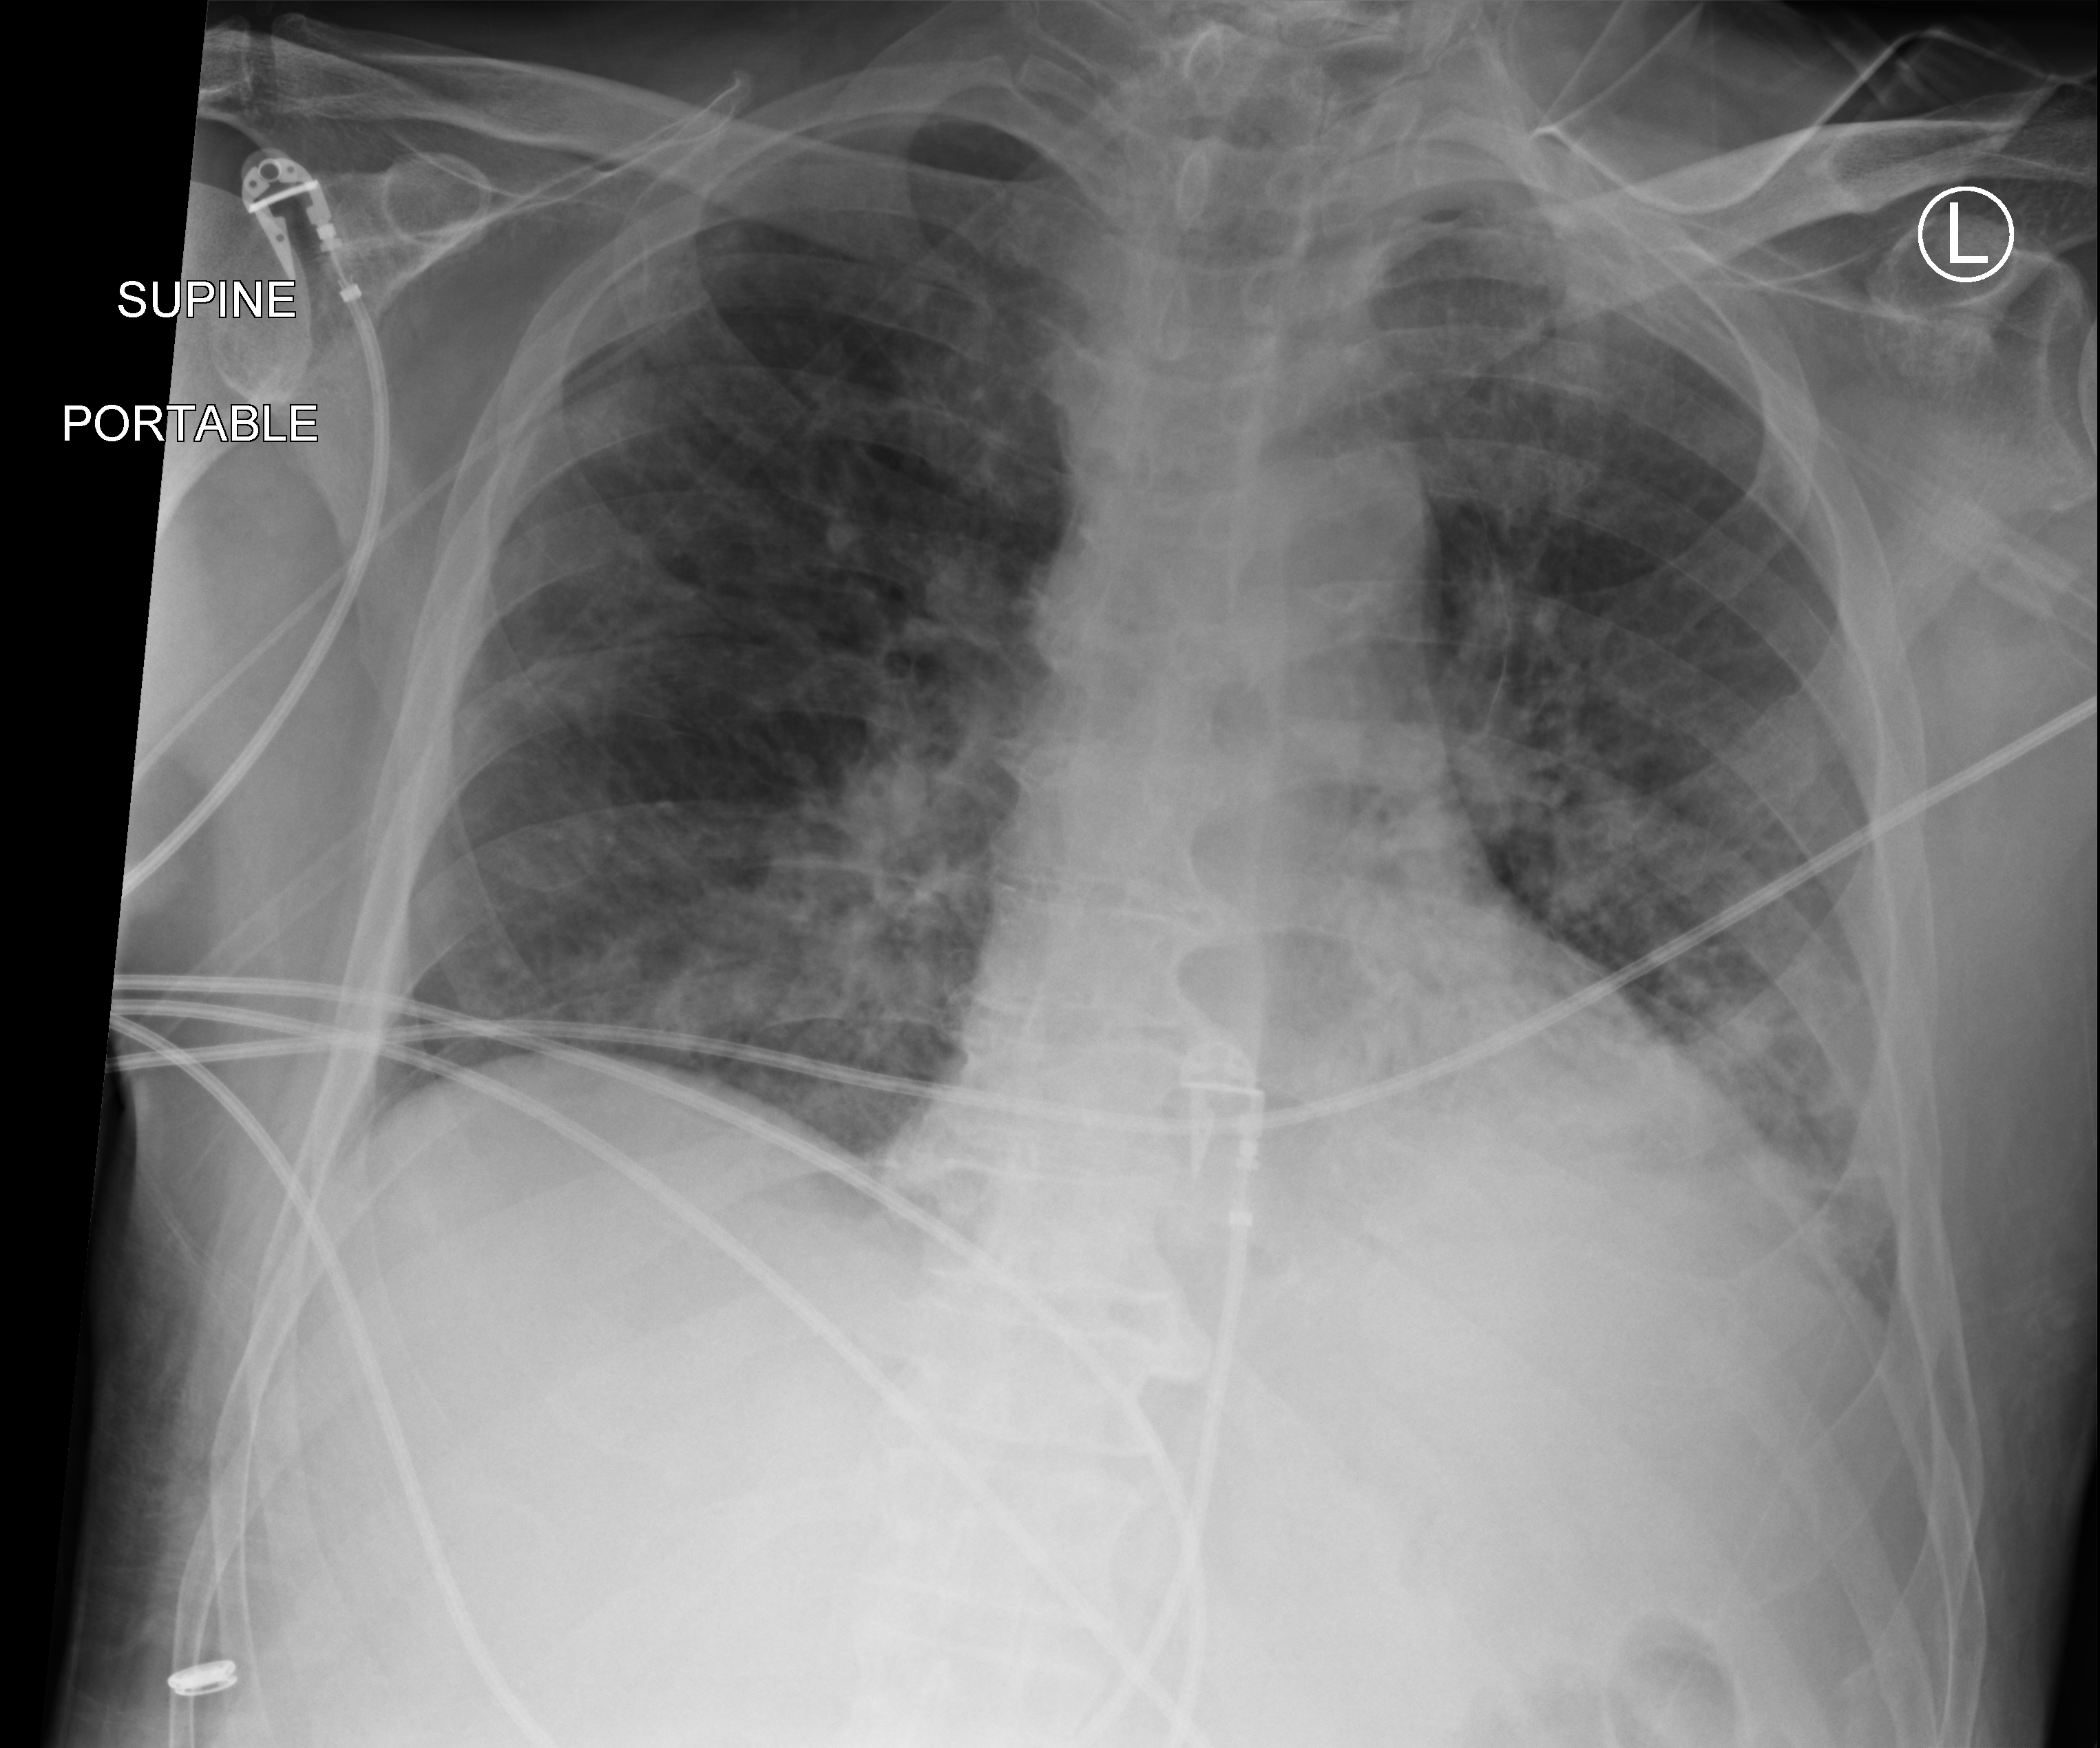
Portable chest radiograph; anteroposterior (AP) projection. Patient hospitalised with COVID-19; male, aged 60–74 years.
From the hospital-stay record, not from the radiograph (when in the stay this image was taken is not recorded):
- length of hospital stay: 35 days
- mechanically ventilated during this hospital stay: yes